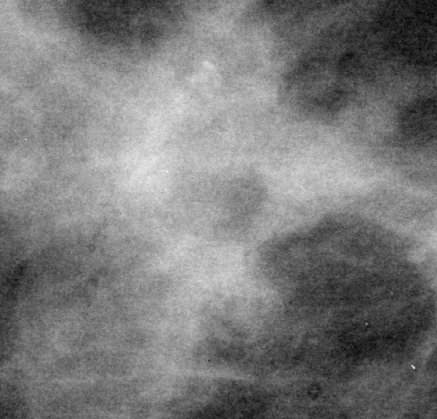
Crop from a digitized film mammogram around one marked abnormality; right breast; MLO view.
- Finding: mass, shape irregular / architectural distortion, margins ill defined / spiculated; BI-RADS assessment category 4; pathology result (as recorded, not read from the image): malignant.